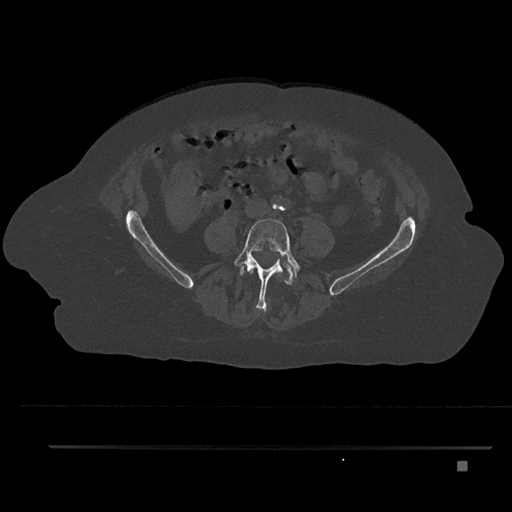
CT including the spine, one axial slice; position 79 of 797 along the scan axis; reconstruction kernel Br40s/3; 120 kVp; bone window (W 1800 / L 400 HU); 512 × 512 image matrix, field of view 437 × 437 mm. Female patient, age 76 years. Case-level facts recorded for this patient, not image findings: primary cancer: lung; vertebrae with lytic lesions (as recorded): T11, L3.
Structures marked on this image (semi-automatically segmented with operator editing):
- L3 vertebra: box from (x=250, y=269) to (x=282, y=278) px
- L4 vertebra: (x=233, y=218)–(x=302, y=311)
- L5 vertebra: (x=240, y=262)–(x=297, y=285)